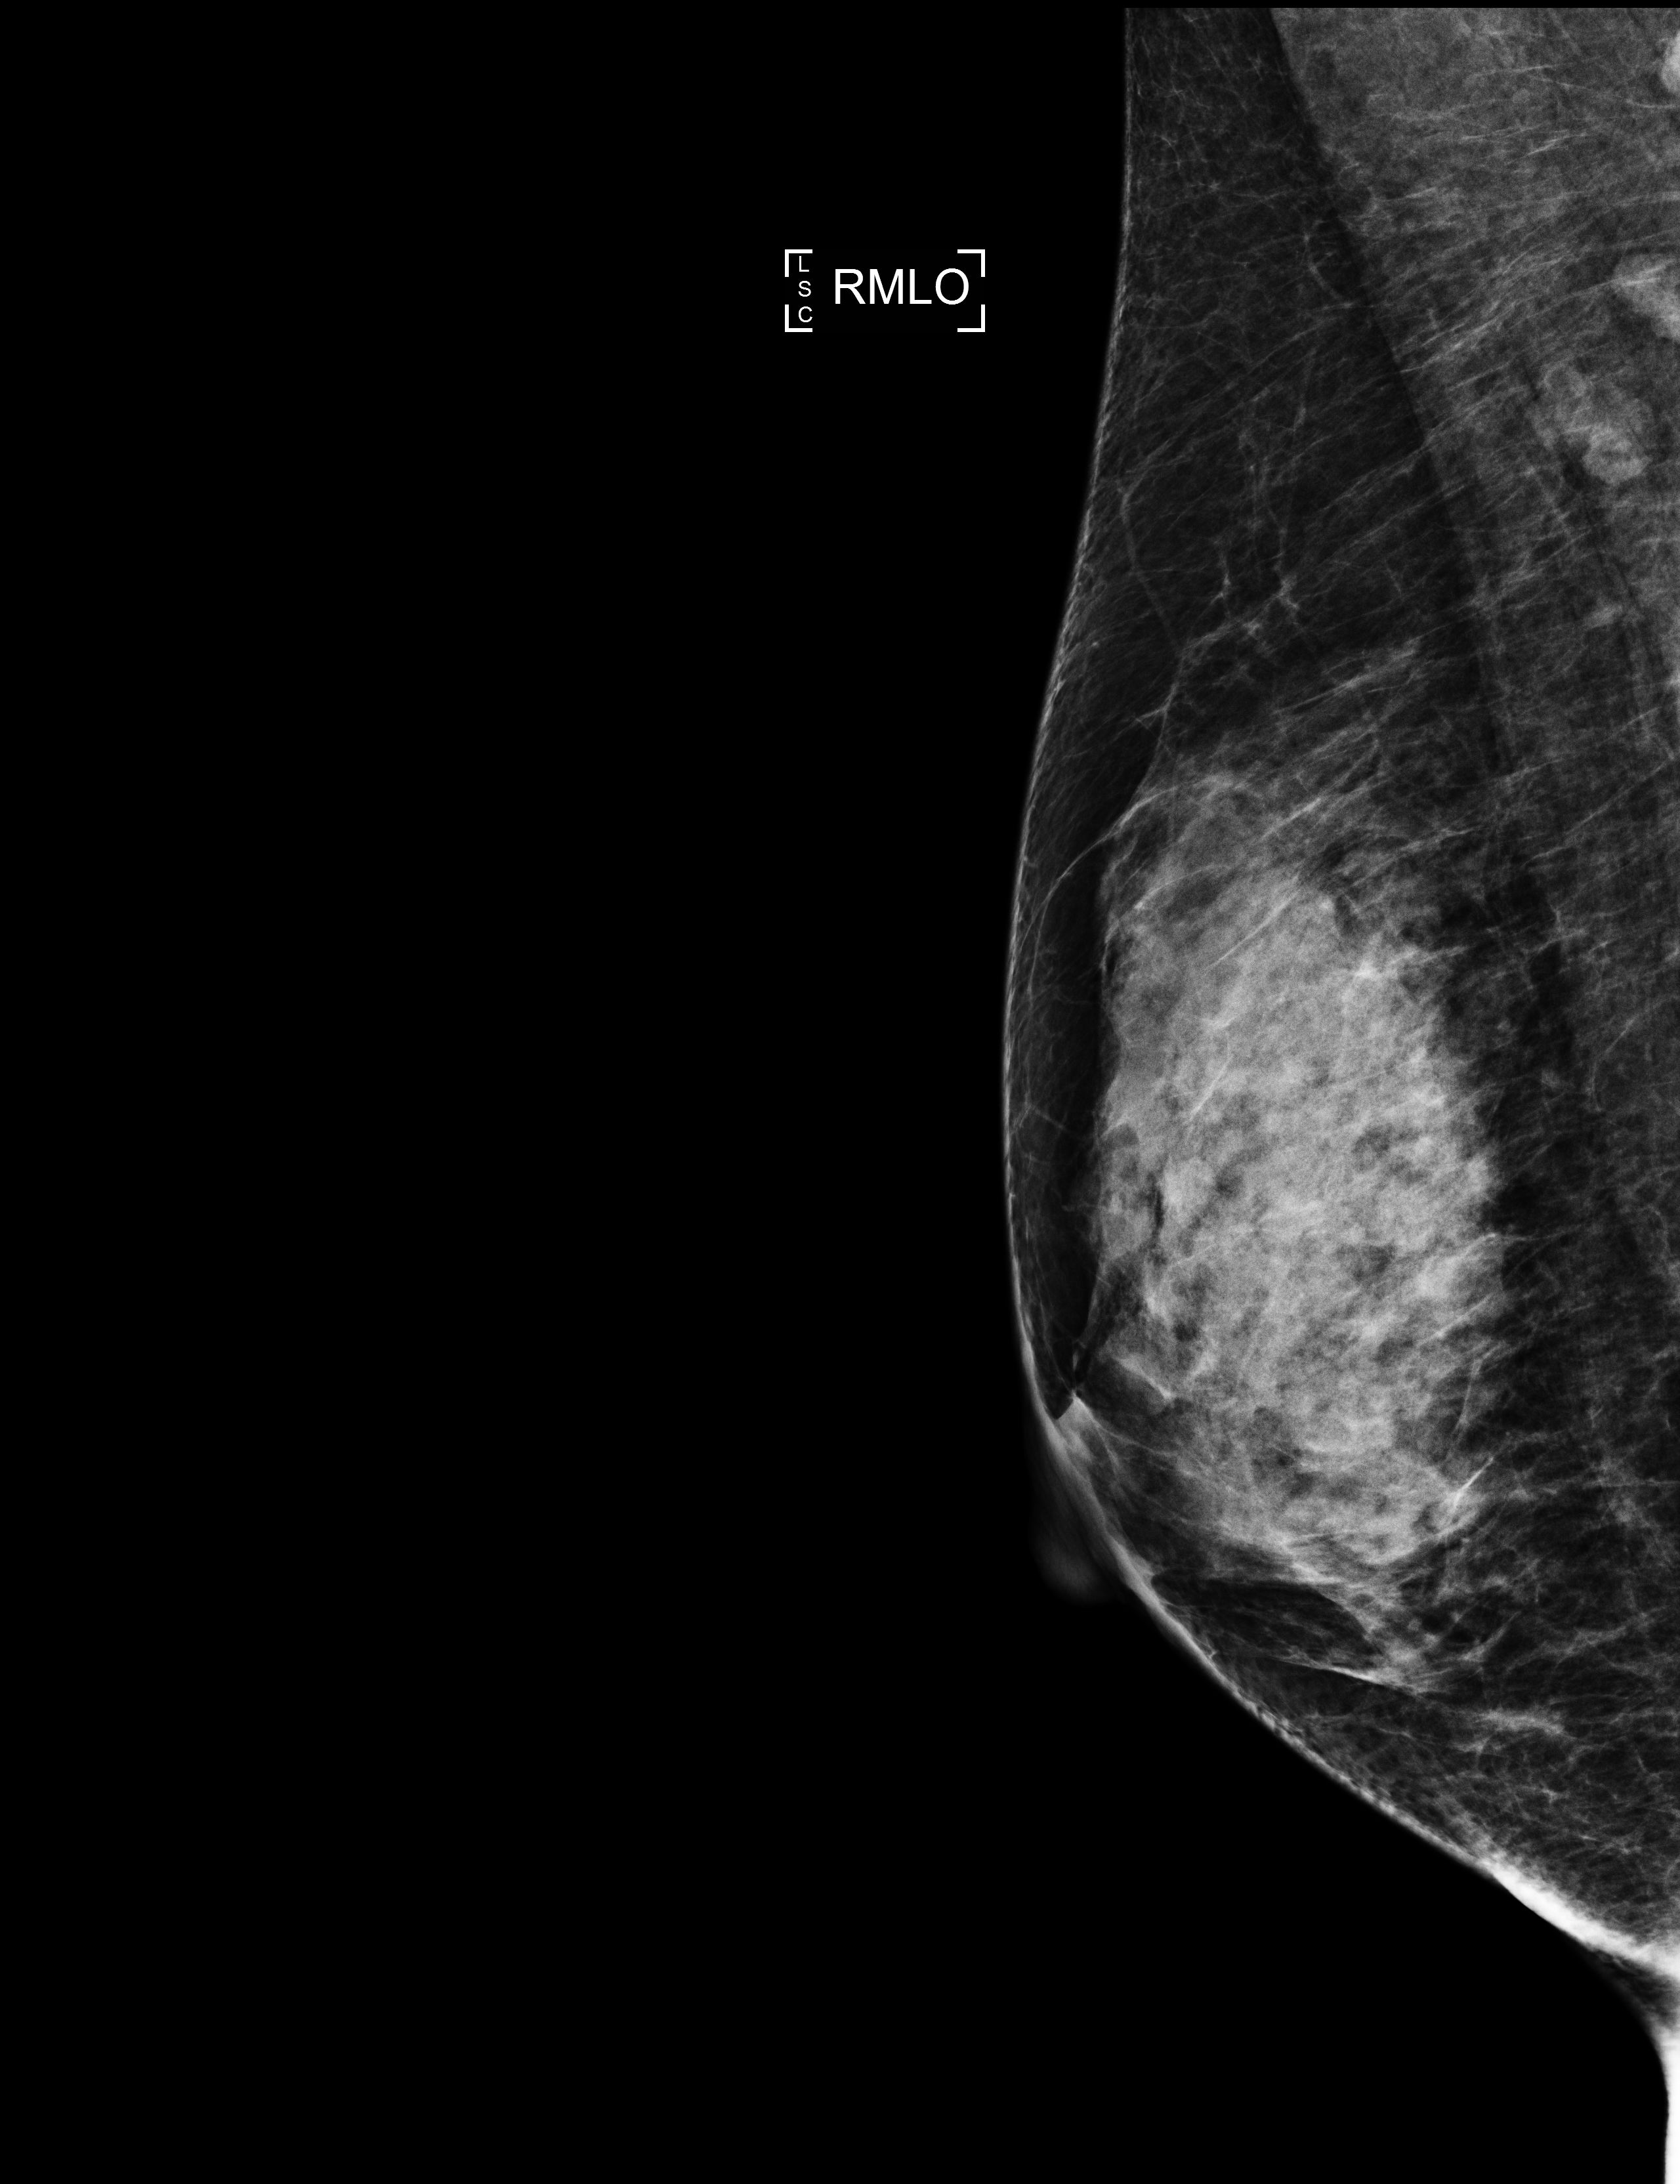
Annual screening mammography examination. Patient aged 51 years (female).
Image type: full-field digital mammogram. Breast: right. Projection: mediolateral oblique (MLO) view.